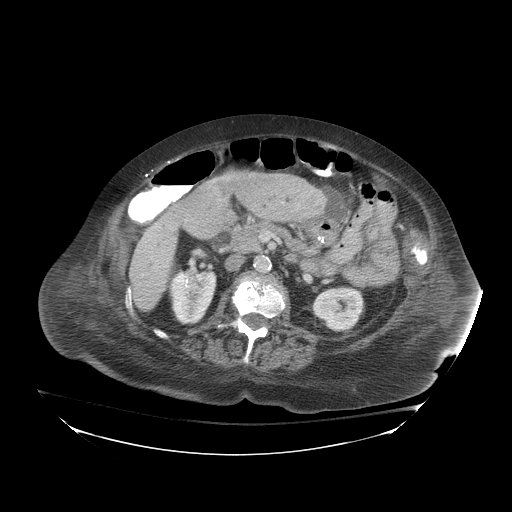
Contrast-enhanced abdominal CT (liver protocol), one axial slice. Slice 30 of 81 in the series (ordered by position). Soft-tissue window (W 400 / L 40 HU). 2.5 mm slice thickness. 512 × 512 image matrix, field of view 500 × 500 mm. Case-level facts recorded for this patient, not image findings: diagnosis: hepatocellular carcinoma (patient treated with transarterial chemoembolisation; whether this scan precedes or follows treatment is not stated here); TNM stage (as recorded): Stage-I.
Annotated regions visible in this slice (semi-automatic segmentation, software-assisted and operator-edited):
- liver parenchyma outside the tumour (the mass and vessels are separate outlines, so this box may not span the whole liver): bounding box [x1, y1, x2, y2] px = [128, 210, 180, 310]
- liver vessels: [128, 289, 131, 295]